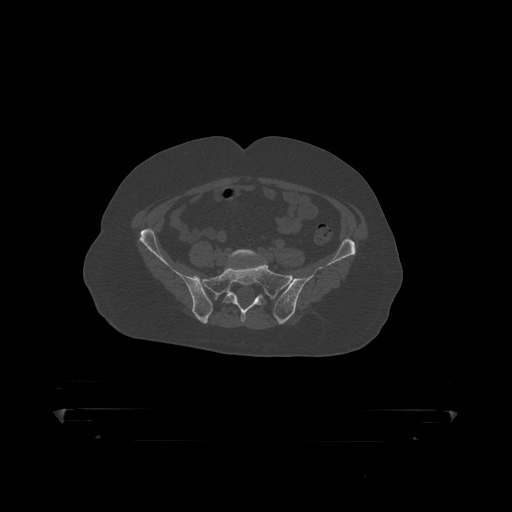
CT including the spine, one axial slice. Position 20 of 390 along the scan axis. Reconstruction kernel STANDARD. 120 kVp. Bone window (W 1800 / L 400 HU). 1.25 mm slice thickness. 512 × 512 image matrix. Patient: male, 60 years. From the clinical record (not read from this slice): primary cancer: prostate.
Structures marked on this image (semi-automatically segmented with operator editing):
- L5 vertebra: box from (x=225, y=249) to (x=263, y=265) px